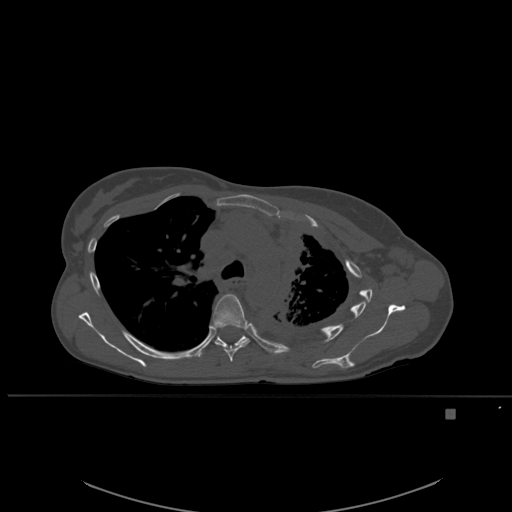
CT including the spine, one axial slice. Slice 393 of 537 in the series (ordered by position). Bone window (W 1800 / L 400 HU). 1.5 mm slice thickness. 512 × 512 image matrix. Patient: female, 45 years. From the clinical record (not read from this slice): primary cancer: lung.
Annotated regions visible in this slice (semi-automatic segmentation, software-assisted and operator-edited):
- T5 vertebra: box from (x=212, y=294) to (x=250, y=362) px
- T6 vertebra: (x=203, y=335)–(x=248, y=355)